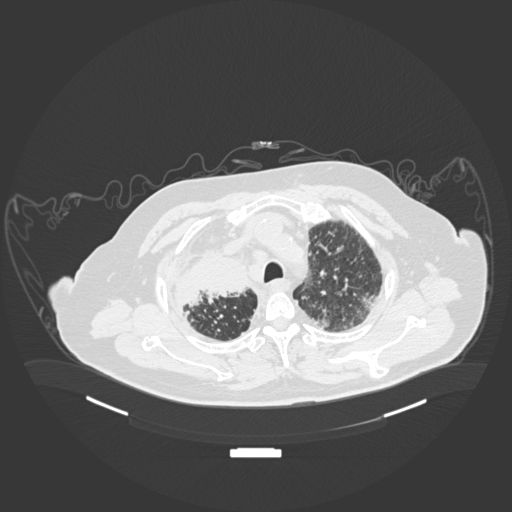
Chest CT, one axial slice; position 152 of 201 along the scan axis; lung window (W 1500 / L -600 HU); 1 mm slice thickness; 512 × 512 image matrix. Patient: male, 69 years. Case-level facts recorded for this patient, not image findings: clinical TNM (as recorded): T4 N3 M1.
Outlined on this slice (rectangle marked by the reading radiologist):
- lung tumour (recorded histology: adenocarcinoma): bounding box [x1, y1, x2, y2] px = [171, 251, 253, 312]